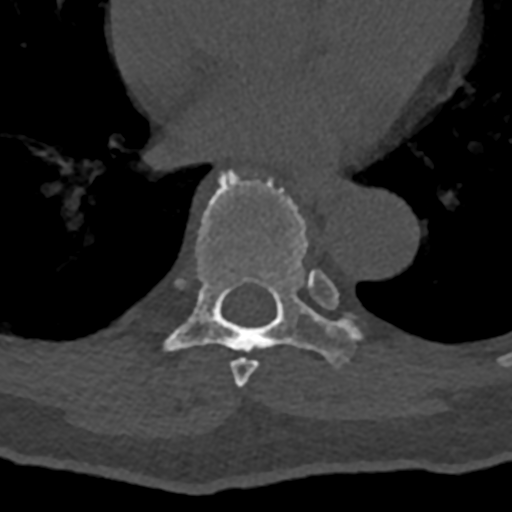
CT including the spine, one axial slice. Slice 718 of 797 in the series (ordered by position). 120 kVp. Bone window (W 1800 / L 400 HU). 512 × 512 image matrix, field of view 160 × 160 mm. Patient: male, 74 years. Case-level facts recorded for this patient, not image findings: primary cancer: renal; vertebrae with lytic lesions (as recorded): T10, L1, L2, L3, L4, L5.
Structures marked on this image (semi-automatically segmented with operator editing):
- T7 vertebra: bounding box [x1, y1, x2, y2] px = [230, 270, 335, 388]
- T8 vertebra: [164, 168, 358, 366]